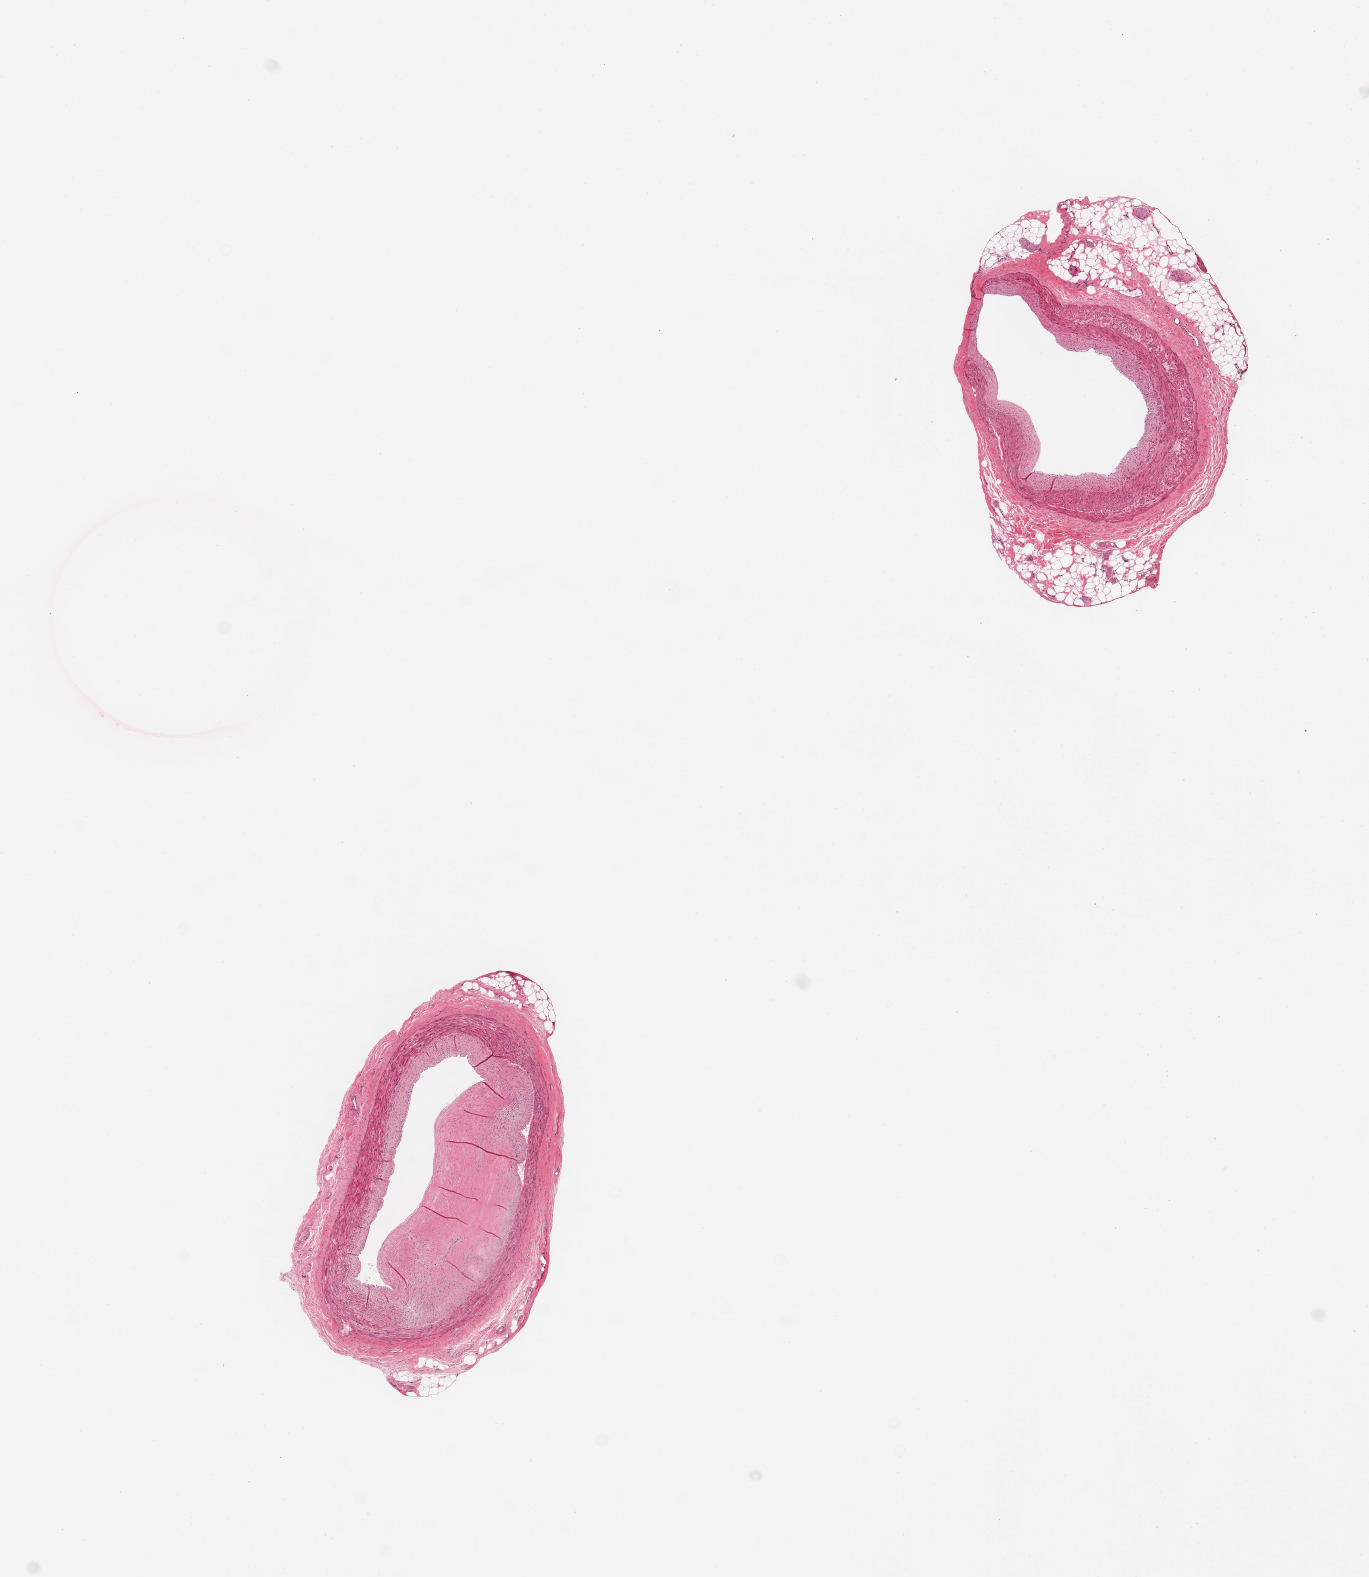
Digitized H&E-stained section — whole scanned area (about 10.8 x 12.5 mm, slide scanned at 20x) shown as a low-resolution overview; PAXgene-fixed paraffin-embedded (PFPE) section; section of coronary artery (target tissue); donor tissue sample. Donor sex: female.
Reviewer comment on this tissue sample: 2 pieces, one with ~60% luminal atherosclerotic occlusion; one with discontinuous adherent fat up to ~0.5mm.